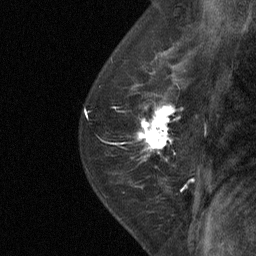
Breast MRI (dynamic contrast-enhanced), one sagittal slice. Slice 45 of 64 in the series (ordered by position). Dynamic contrast-enhanced study with each time point stored as its own series, time point 2 of 4 at this slice position (early post-contrast, ordered by acquisition time). 1.5 T. TE 4.8 ms, TR 27 ms. 256 × 256 image matrix. Female patient, age 50 years. Case-level facts recorded for this patient, not image findings: setting: breast cancer imaged before/during neoadjuvant chemotherapy; receptor status: HER2-positive.
Outlined on this slice (semi-automatic segmentation, software-assisted and operator-edited):
- analysis volume of interest (the breast-tissue region the enhancement analysis was run in; not a lesion): bounding box <123,91,184,177> (left, top, right, bottom; pixels)
- tumour enhancement mask (voxels above the 90 % enhancement threshold inside the analysis volume of interest): <136,103,182,149>